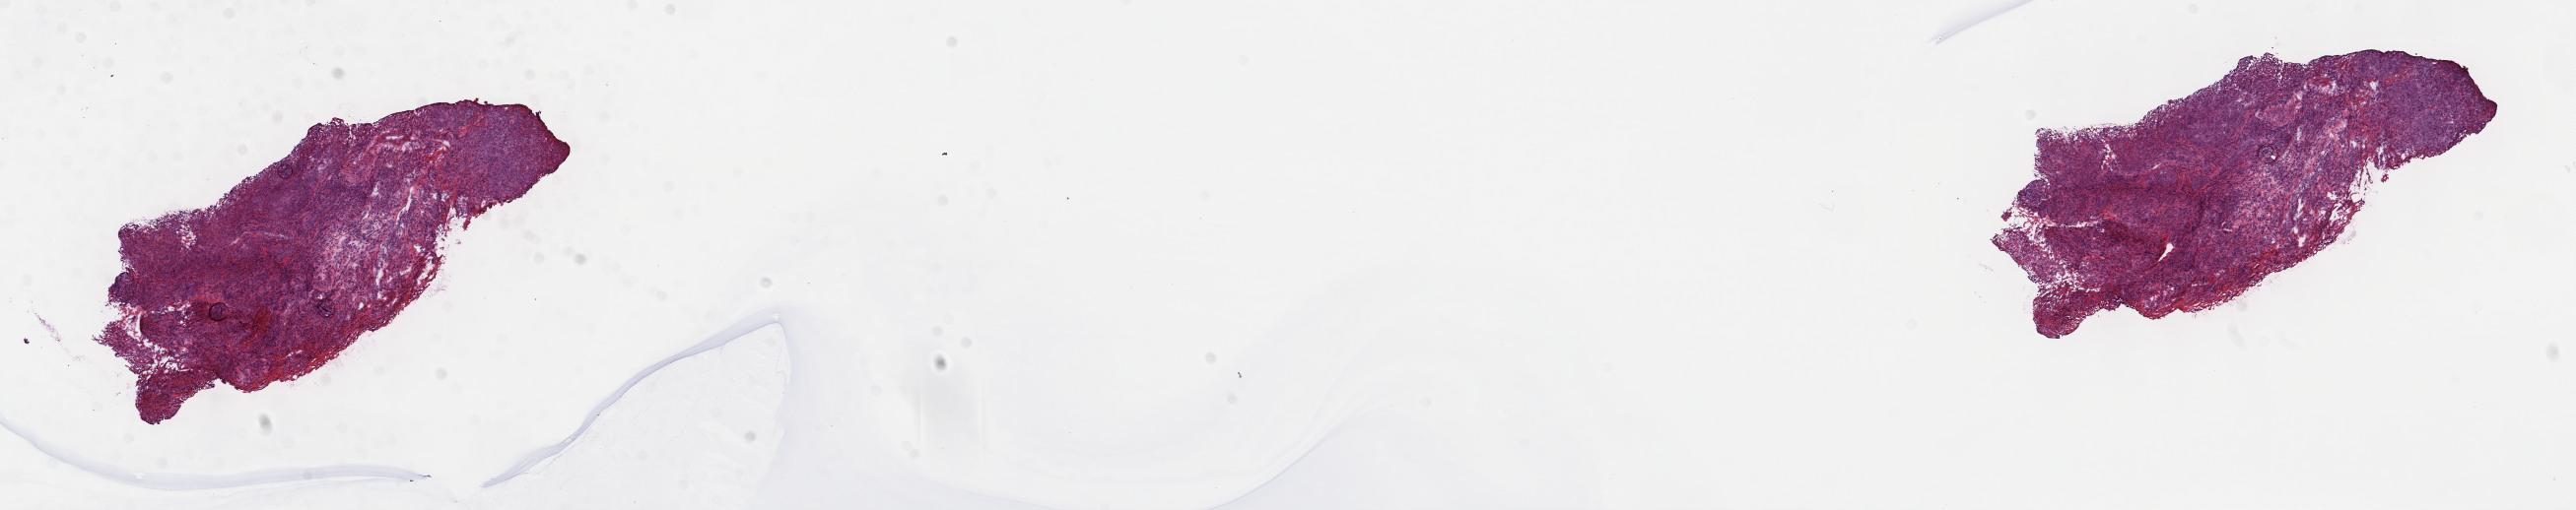
Digitized H&E tissue section (whole slide) — low-resolution overview of the scanned area, about 21.1 x 4.2 mm (slide scanned at 40x). Frozen section from the top of the tissue portion. Mesothelium, primary tumour sample. Male patient; age at initial diagnosis 79 years. Pathologist review of this section (percent, as recorded): tumour cells 80%, tumour nuclei 80%, normal cells 0%, stromal cells 20%, necrosis 0%. Inflammatory infiltration, as recorded: lymphocyte infiltration 70%, monocyte infiltration 10%, neutrophil infiltration 10%.
• AJCC pathologic stage: I
• laterality: right
• histologic diagnosis: Mesothelioma, biphasic, malignant (pleura, NOS)